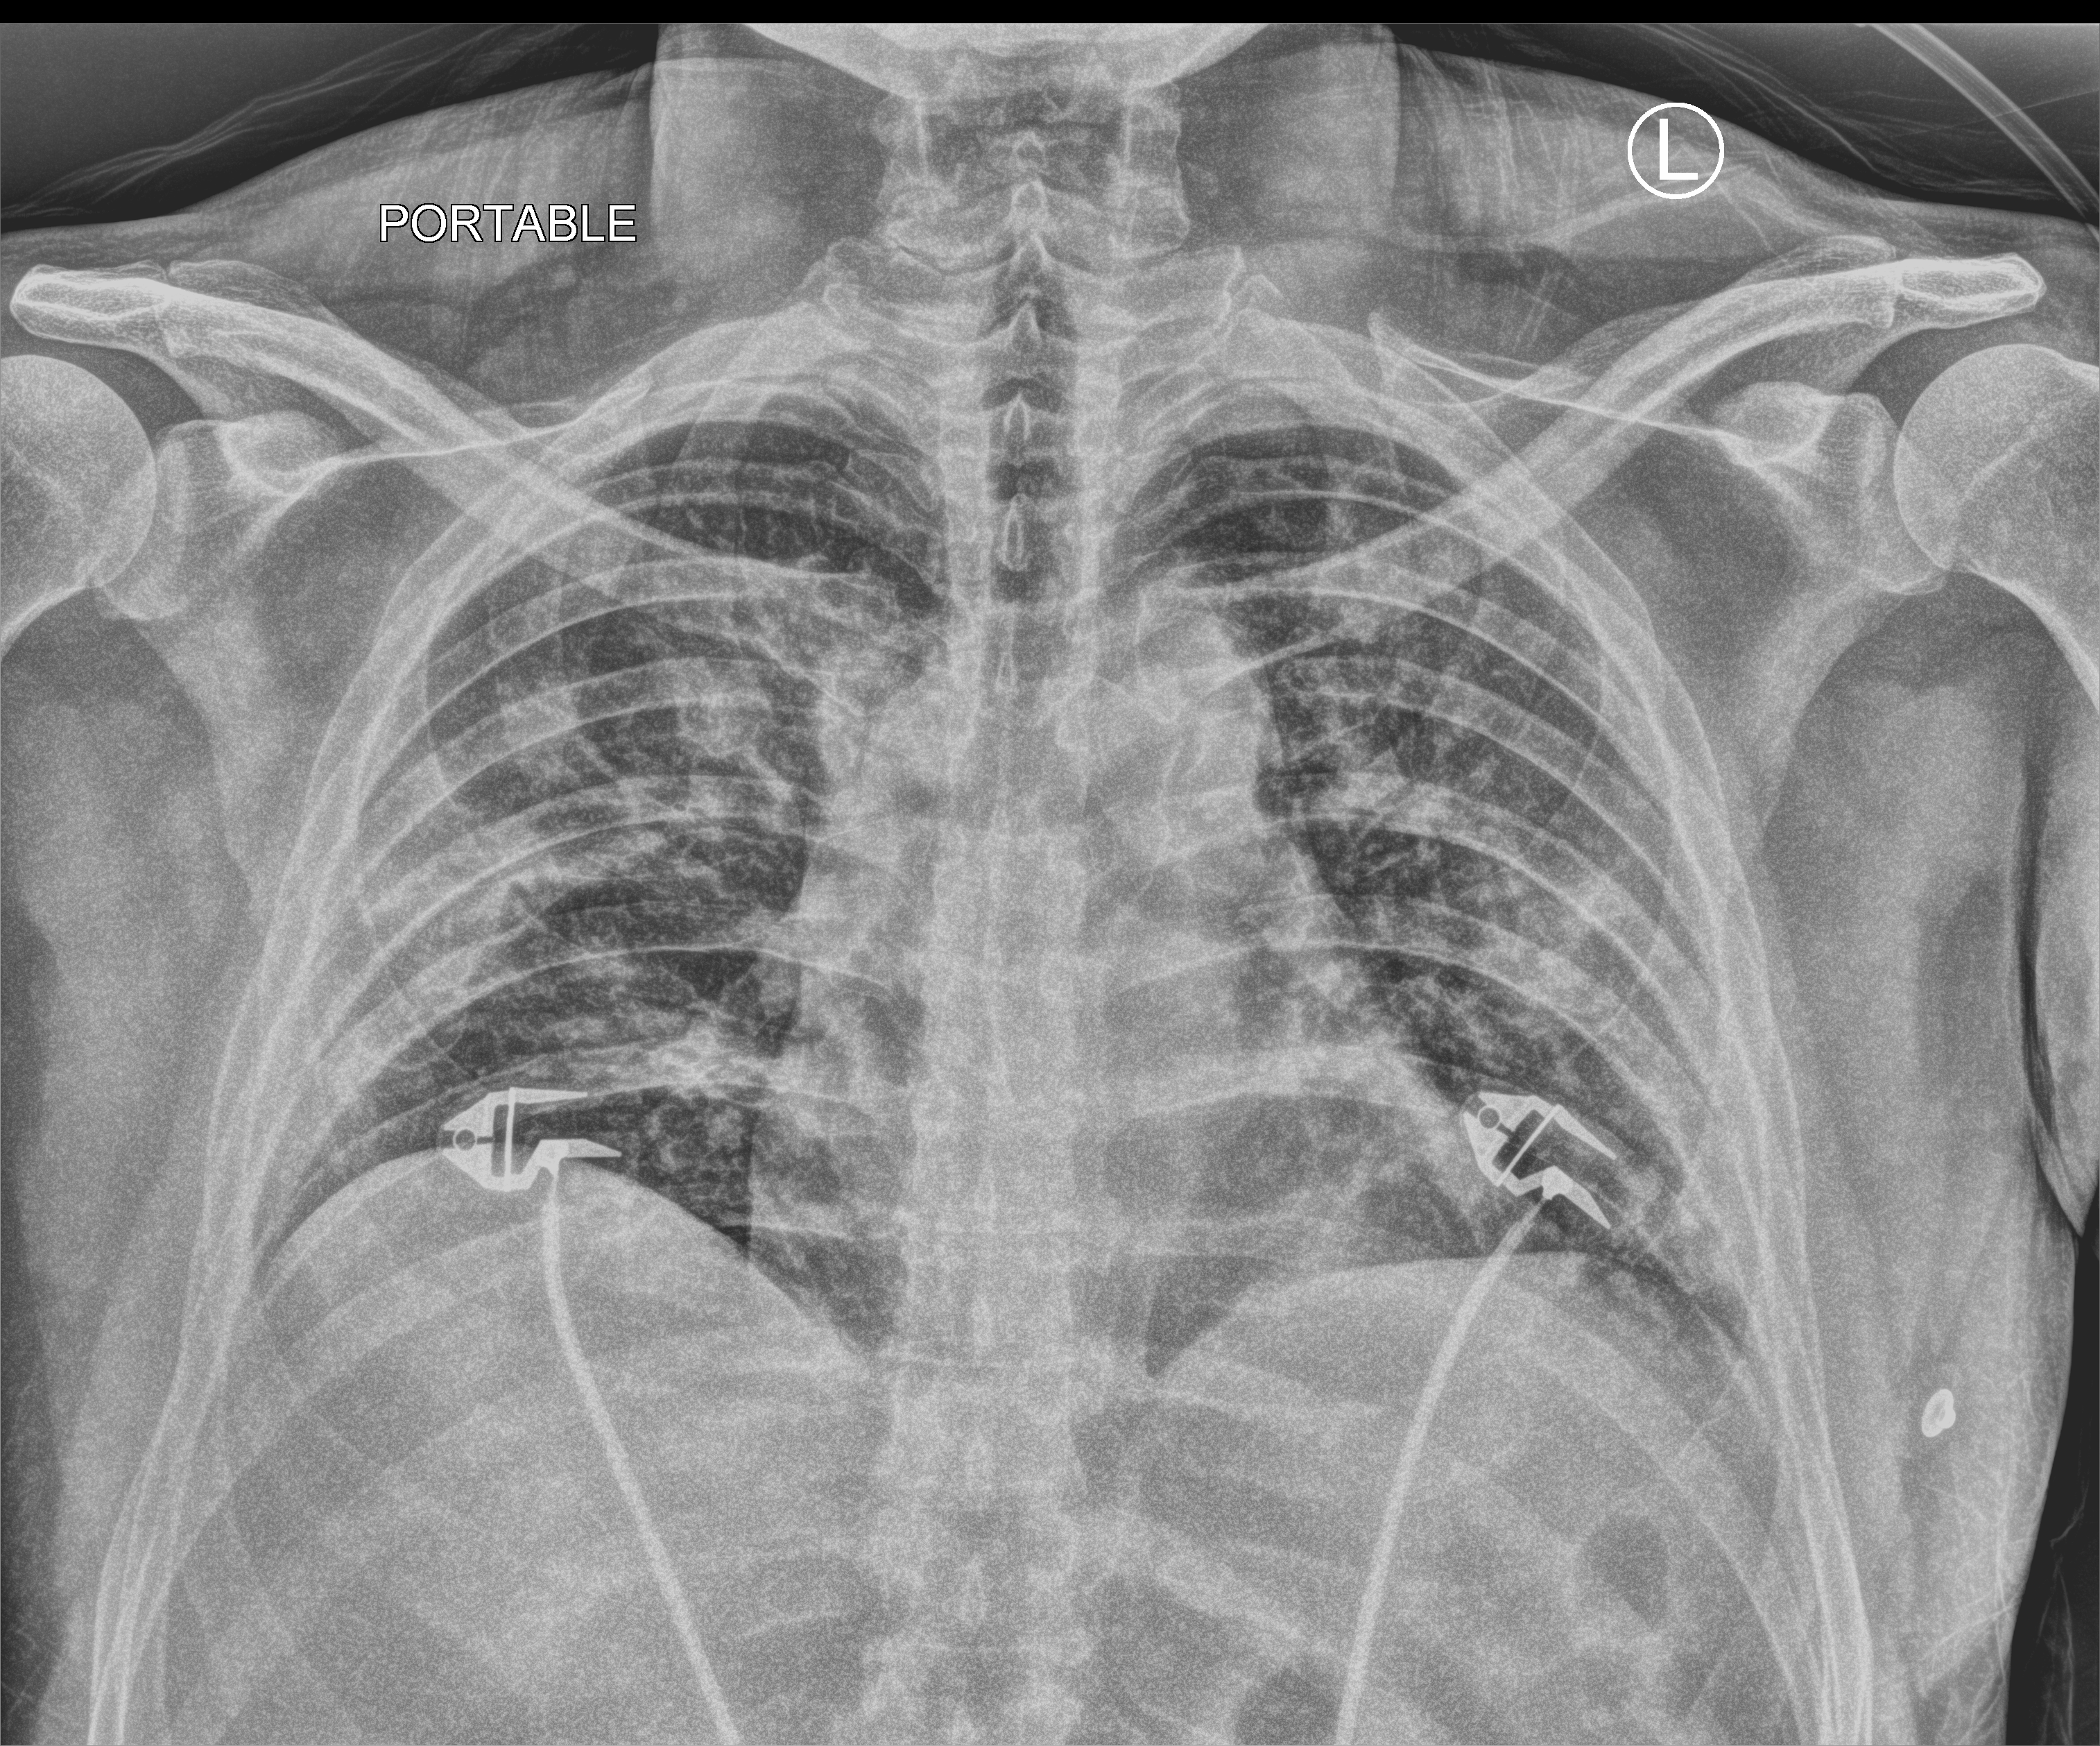
Chest X-ray (portable); anteroposterior (AP) projection. Patient hospitalised with COVID-19; male, aged 18–59 years.
Admission-level facts for this patient (not findings on this image; timing relative to this image not recorded):
- mechanically ventilated during this hospital stay: no
- diabetes (admission record): no
- admitted to intensive care during this hospital stay: yes